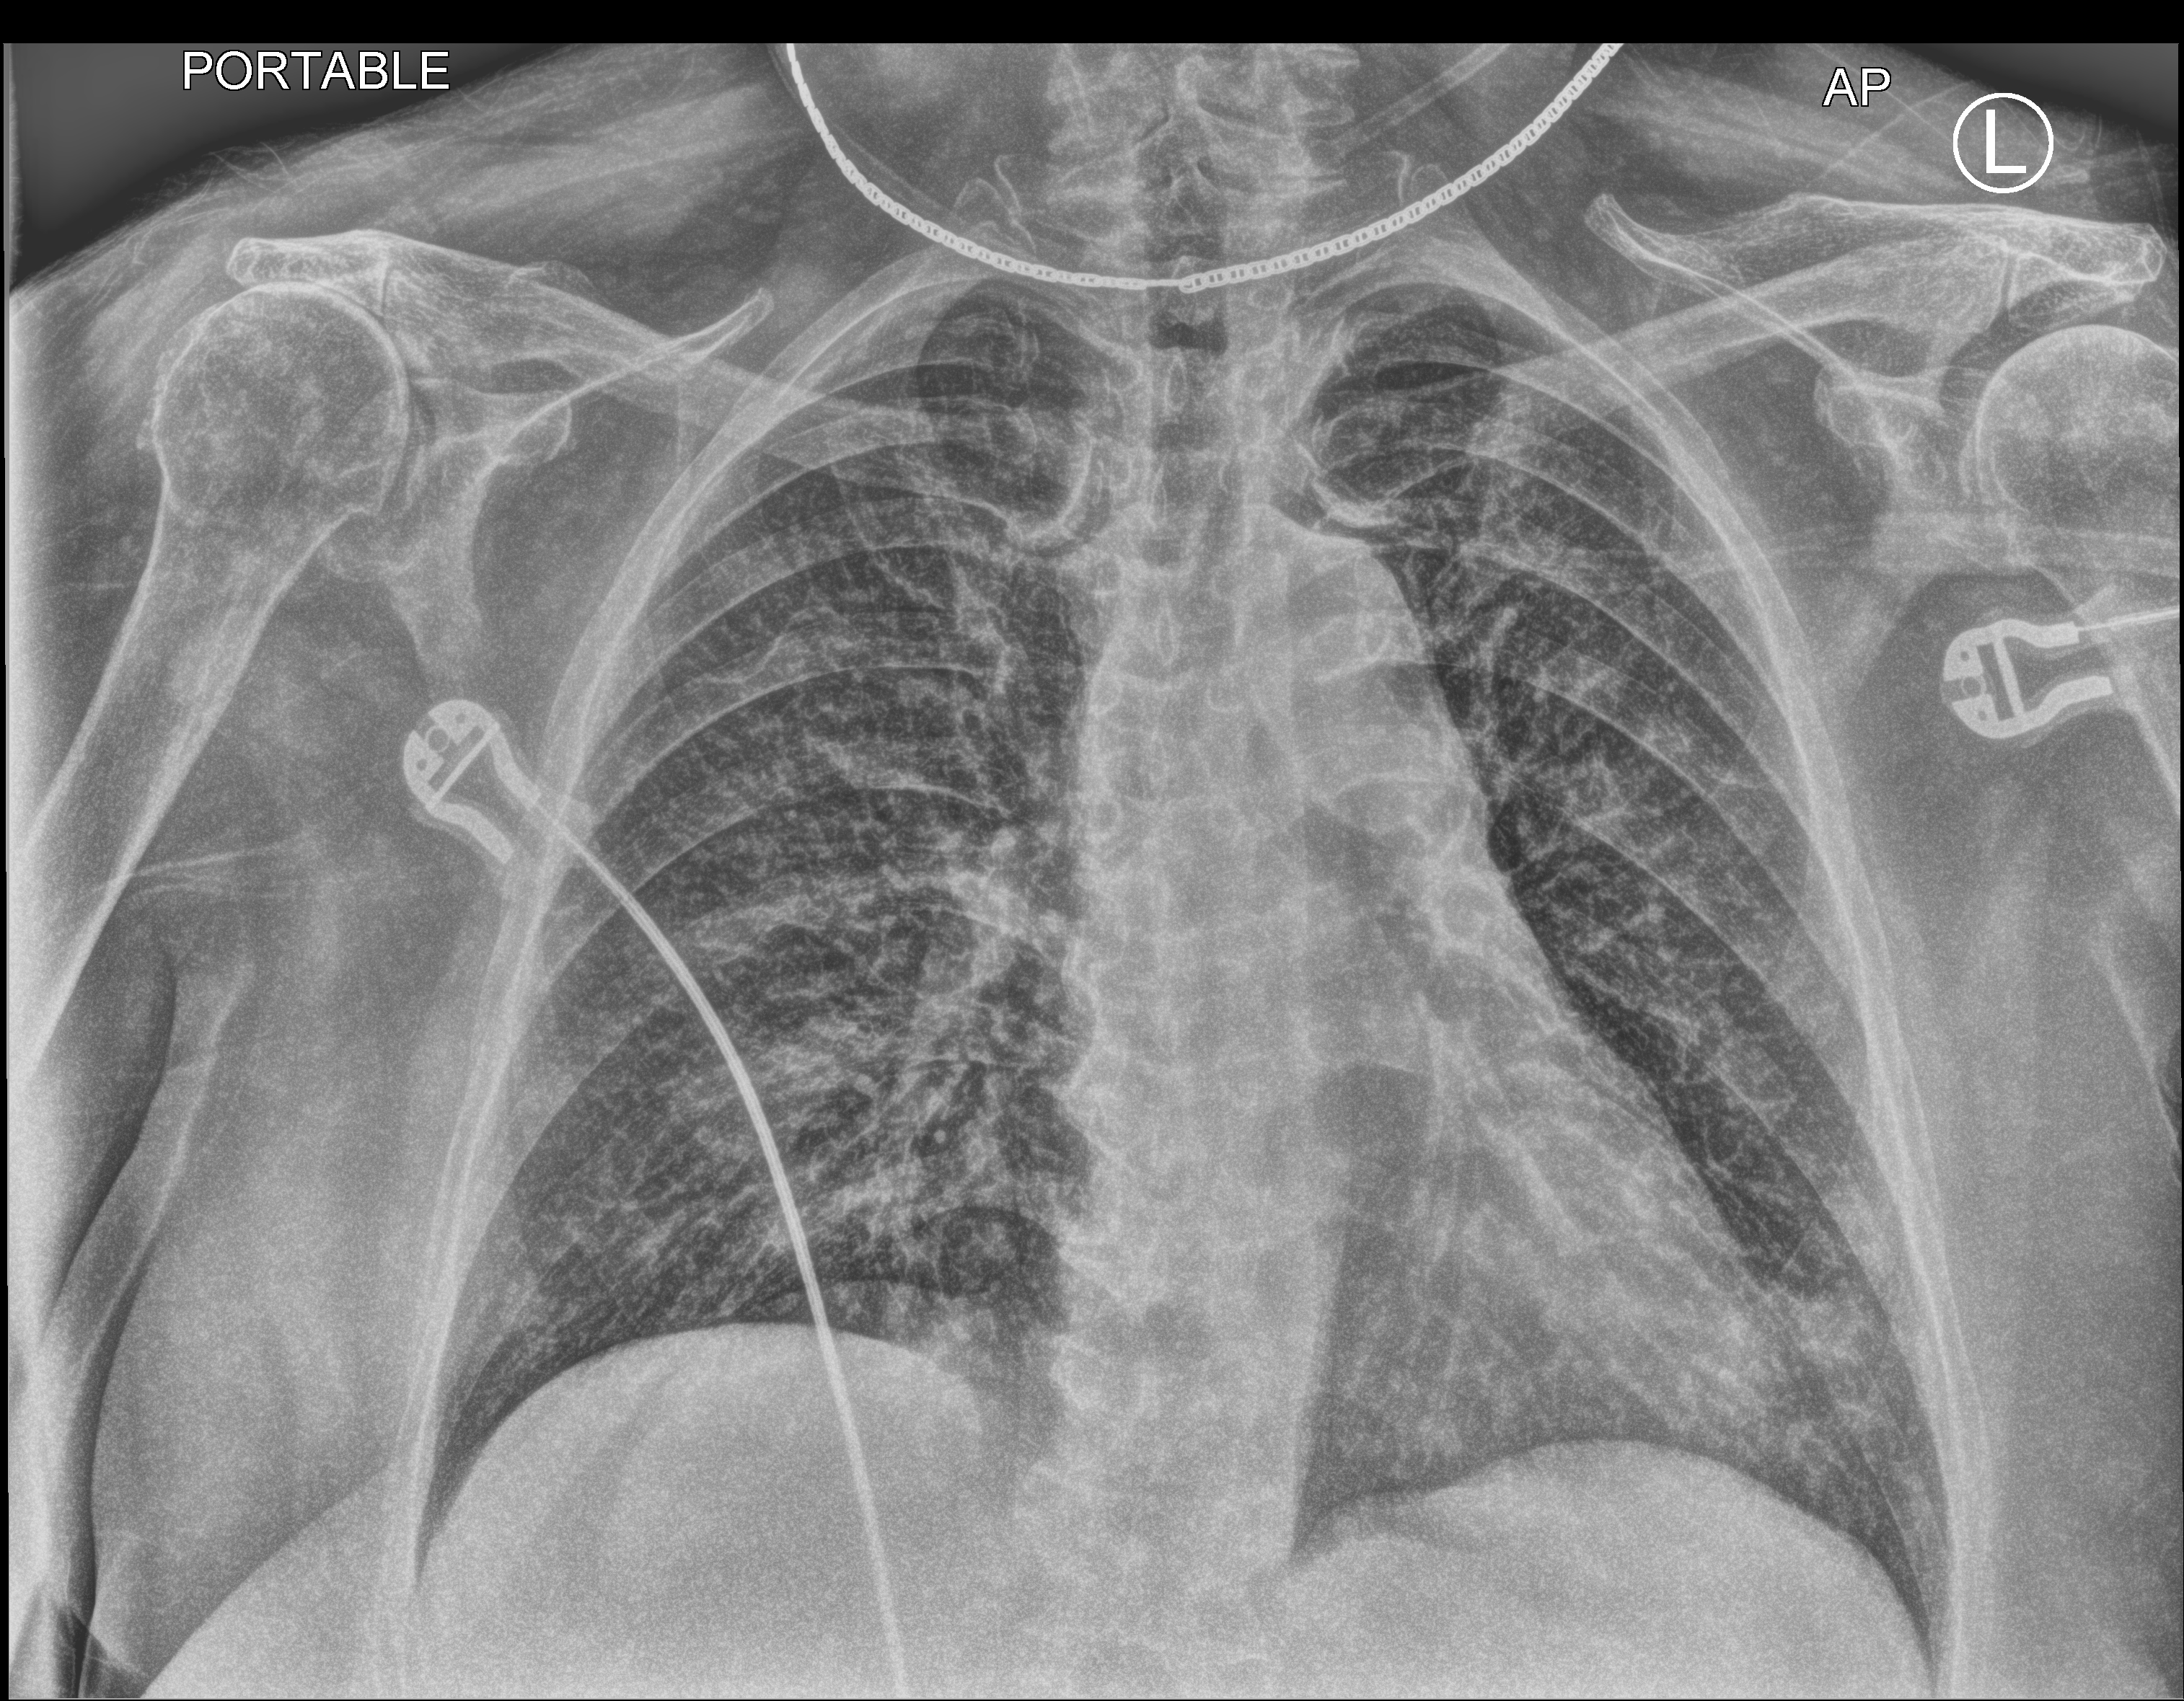
Chest X-ray (portable); anteroposterior (AP) projection. Patient hospitalised with COVID-19; female, aged 60–74 years.
From the hospital-stay record, not from the radiograph (when in the stay this image was taken is not recorded): admitted to intensive care during this hospital stay: no.